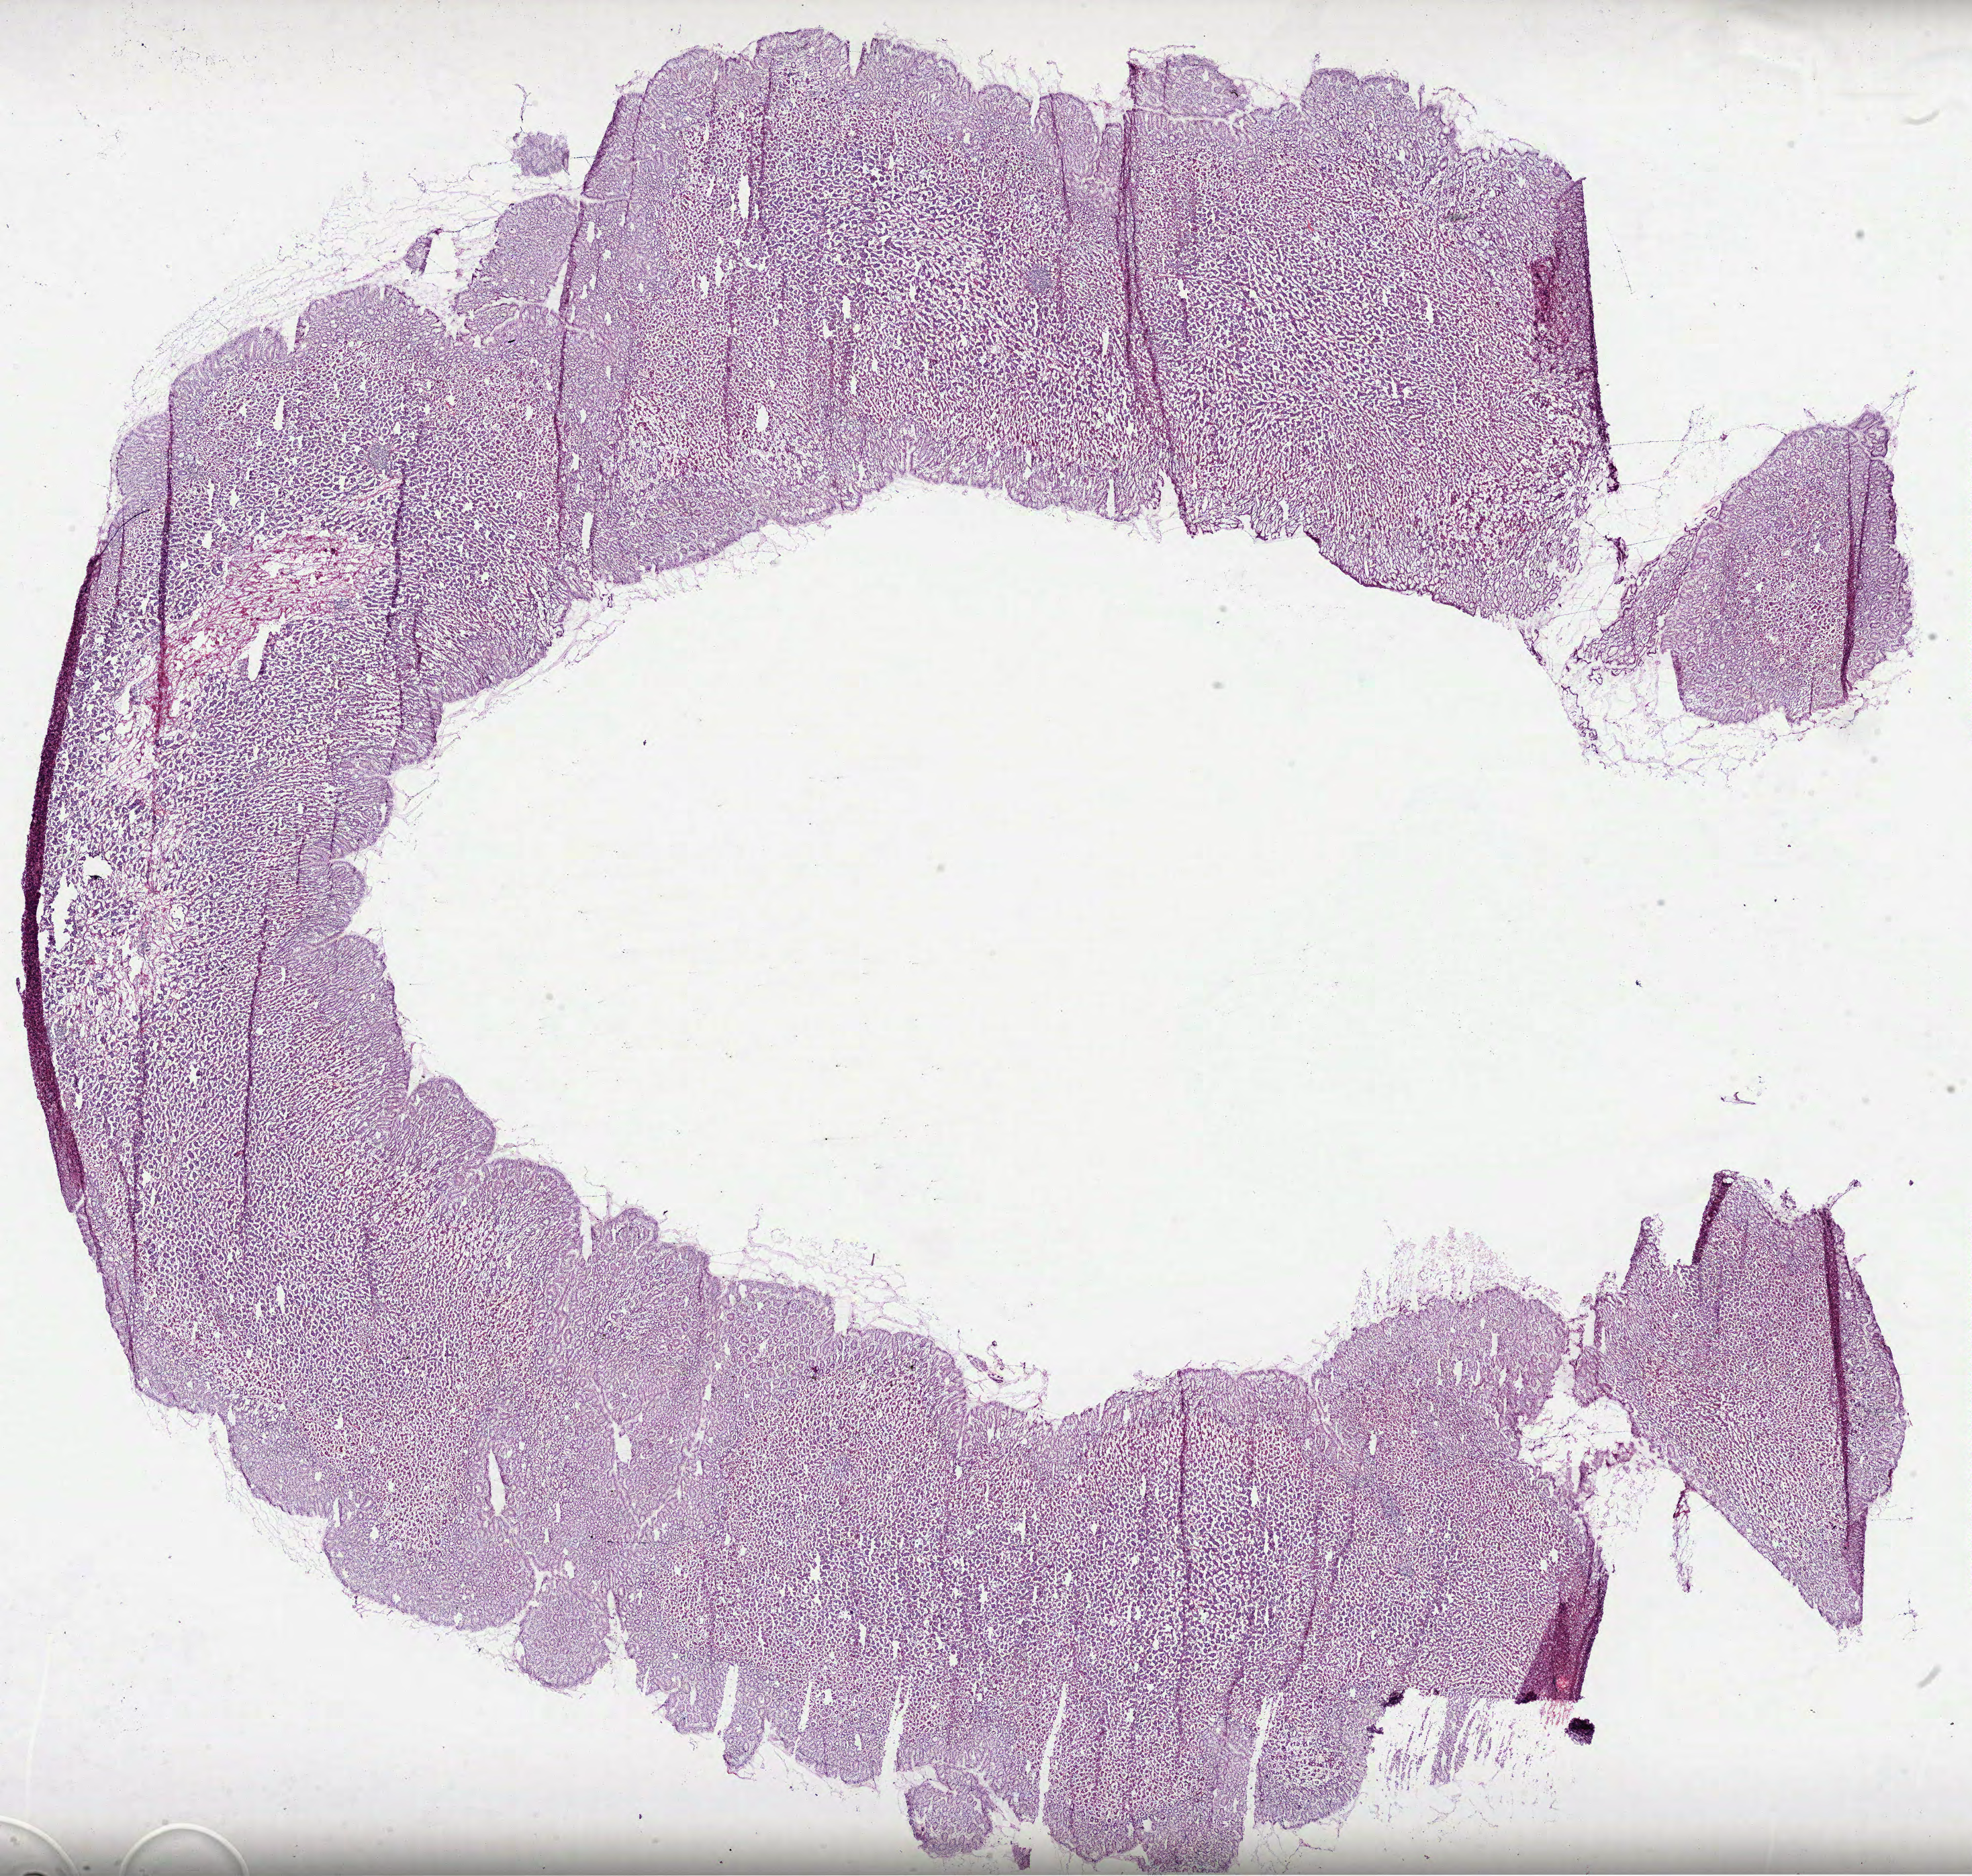
Whole-slide histology image, H&E — low-resolution overview of the scanned area, about 23.7 x 22.5 mm (slide scanned at 40x); frozen section from the top of the tissue portion; solid tissue normal (non-tumour tissue) sample from the stomach. Male patient; age at initial diagnosis 59 years.
* this section: solid tissue normal sample (biorepository sample class)
* patient diagnosis: Mucinous adenocarcinoma (cardia, NOS)